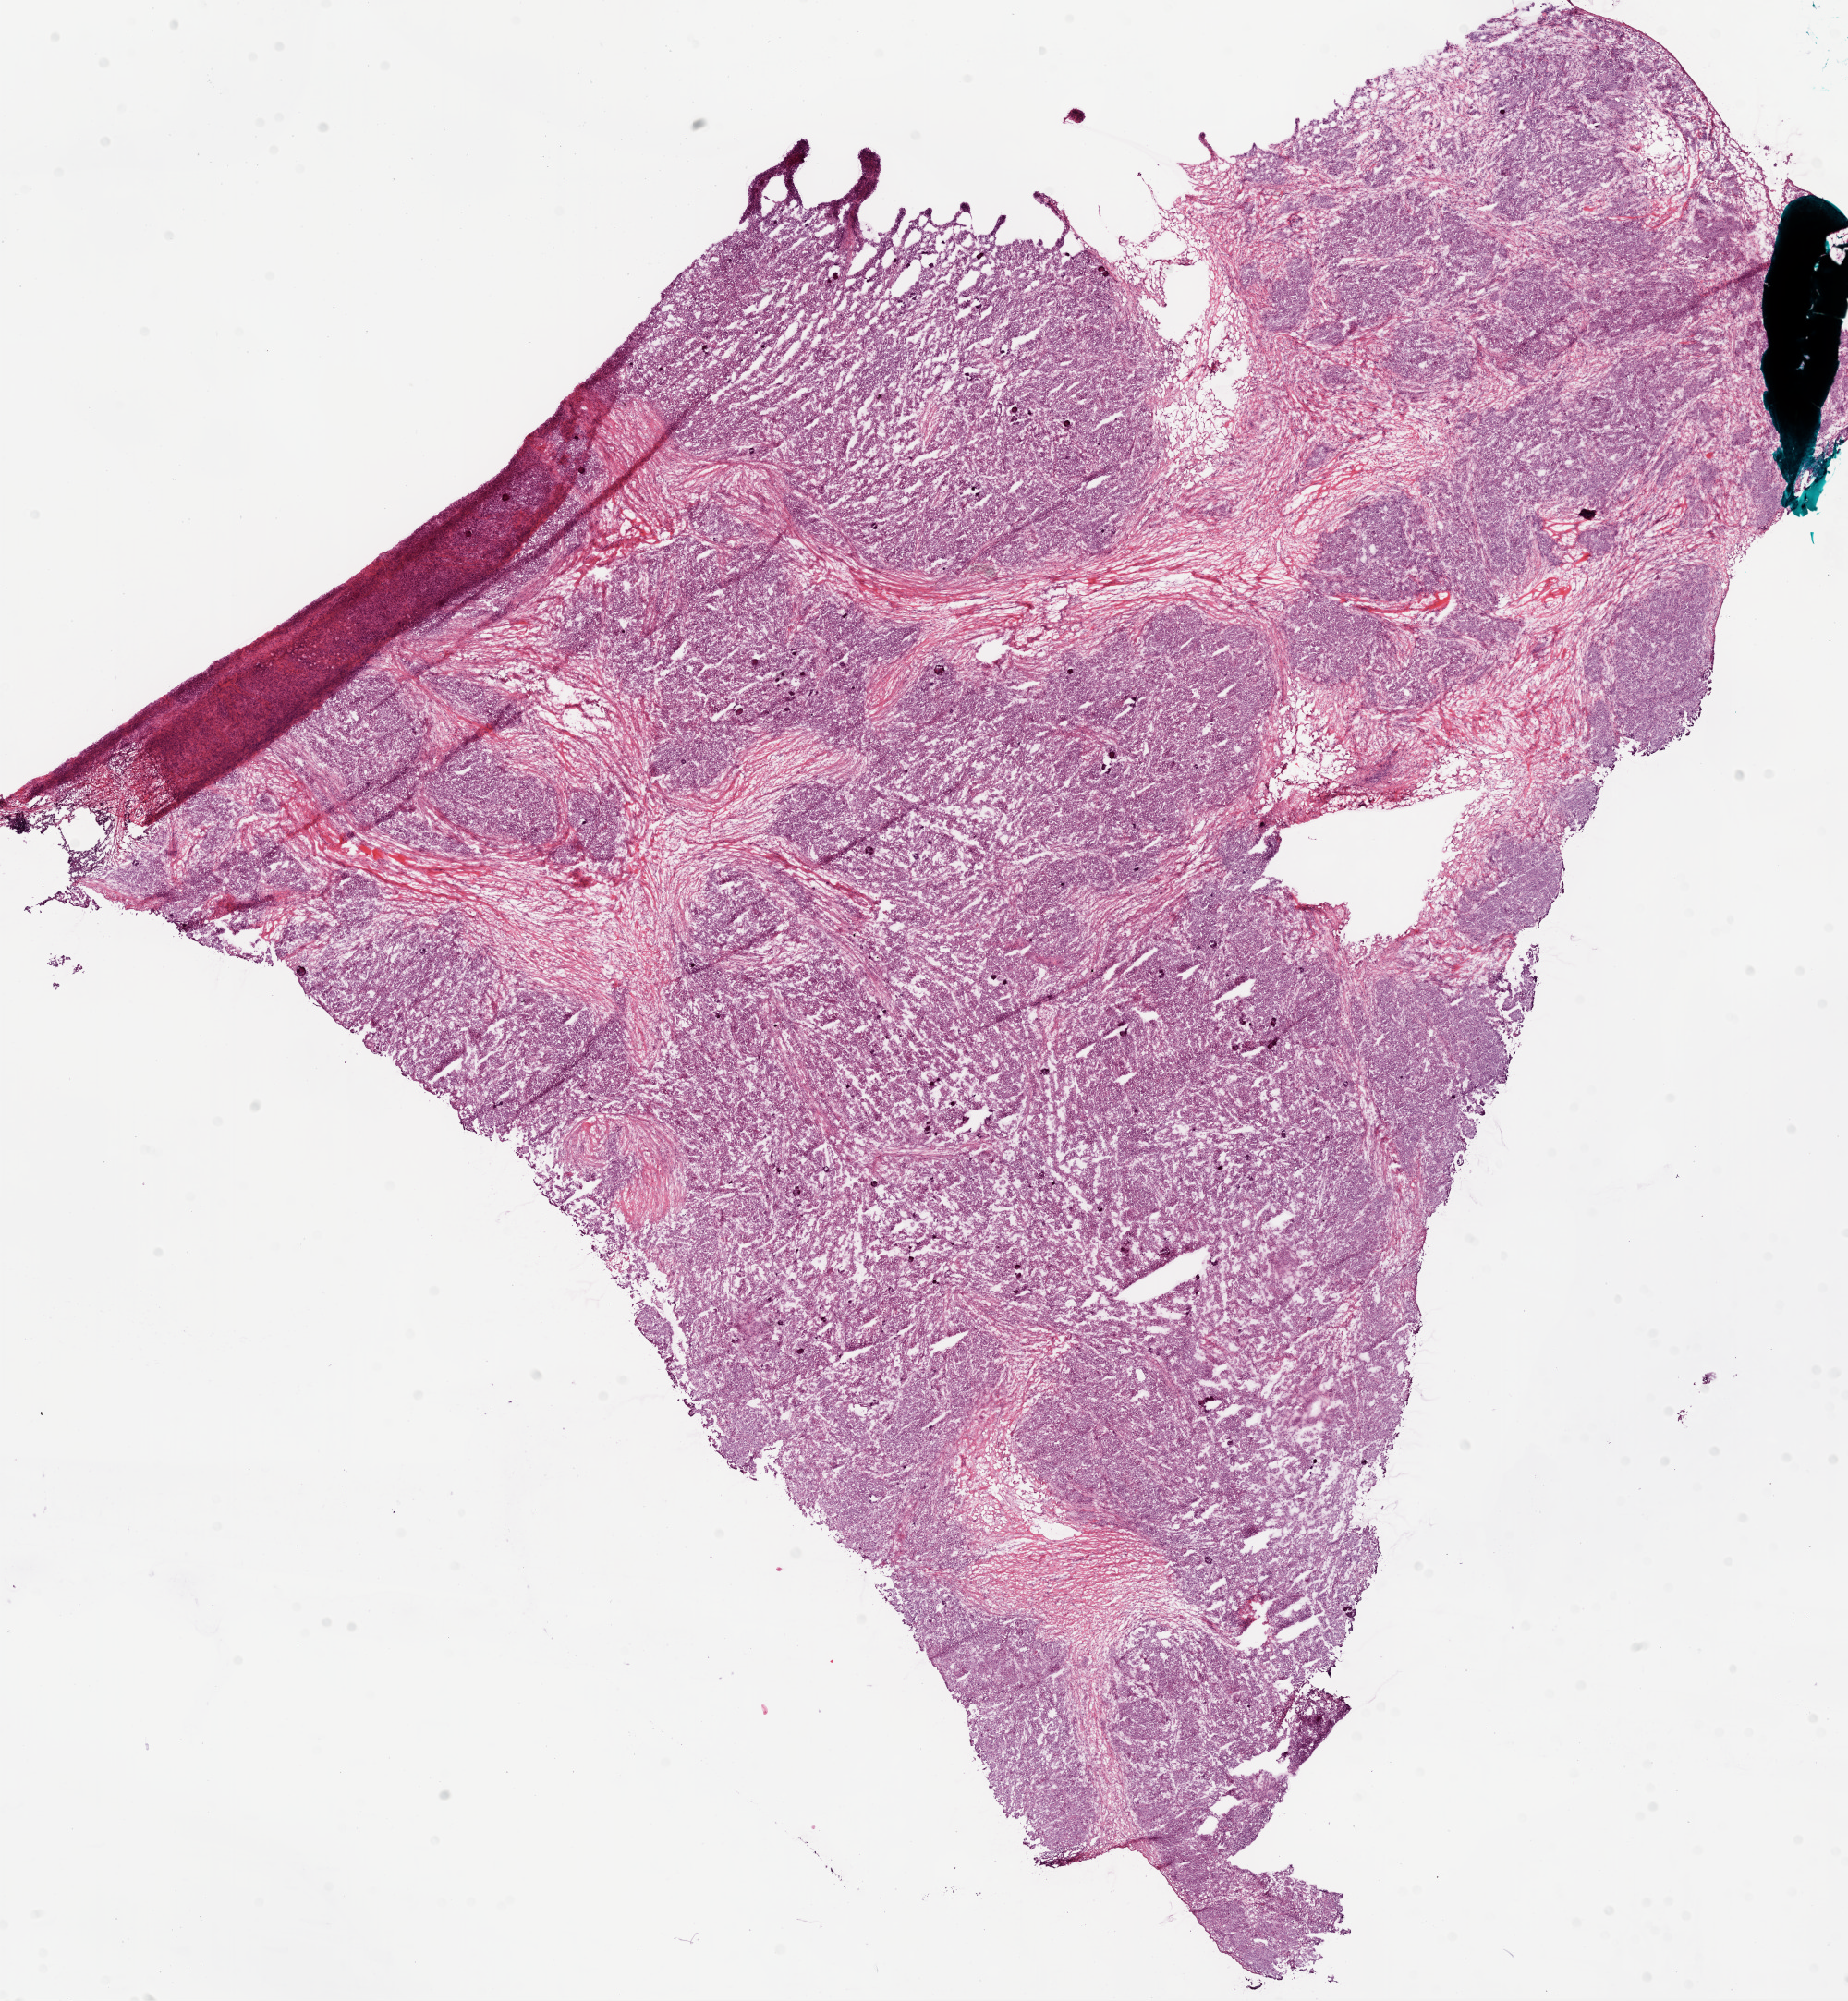
Whole-slide histology image, H&E, shown as a low-resolution overview of the whole scanned area (about 16.0 x 17.4 mm, slide scanned at 20x); frozen section from the bottom of the tissue portion; ovary, primary tumour sample. Female, age 81 years at initial diagnosis. Histologic grade: G3 (poorly differentiated). Slide review estimates, as recorded: tumour cells 90%, tumour nuclei 90%, normal cells 0%, stromal cells 10%, necrosis 0%.
FIGO stage: IIIC. Diagnosis: Serous cystadenocarcinoma, NOS.